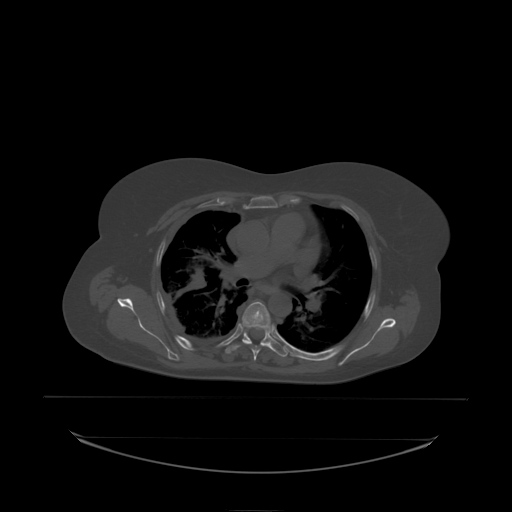
CT including the spine, one axial slice. Bone window (W 1800 / L 400 HU). 2.5 mm slice thickness. 512 × 512 image matrix. Female patient, age 53 years. From the clinical record (not read from this slice): primary cancer: lung; vertebrae with lytic lesions (as recorded): T7, L1.
Structures marked on this image (semi-automatic segmentation, software-assisted and operator-edited):
- T5 vertebra: box from (x=245, y=302) to (x=266, y=324) px
- T6 vertebra: (x=243, y=308)–(x=271, y=338)